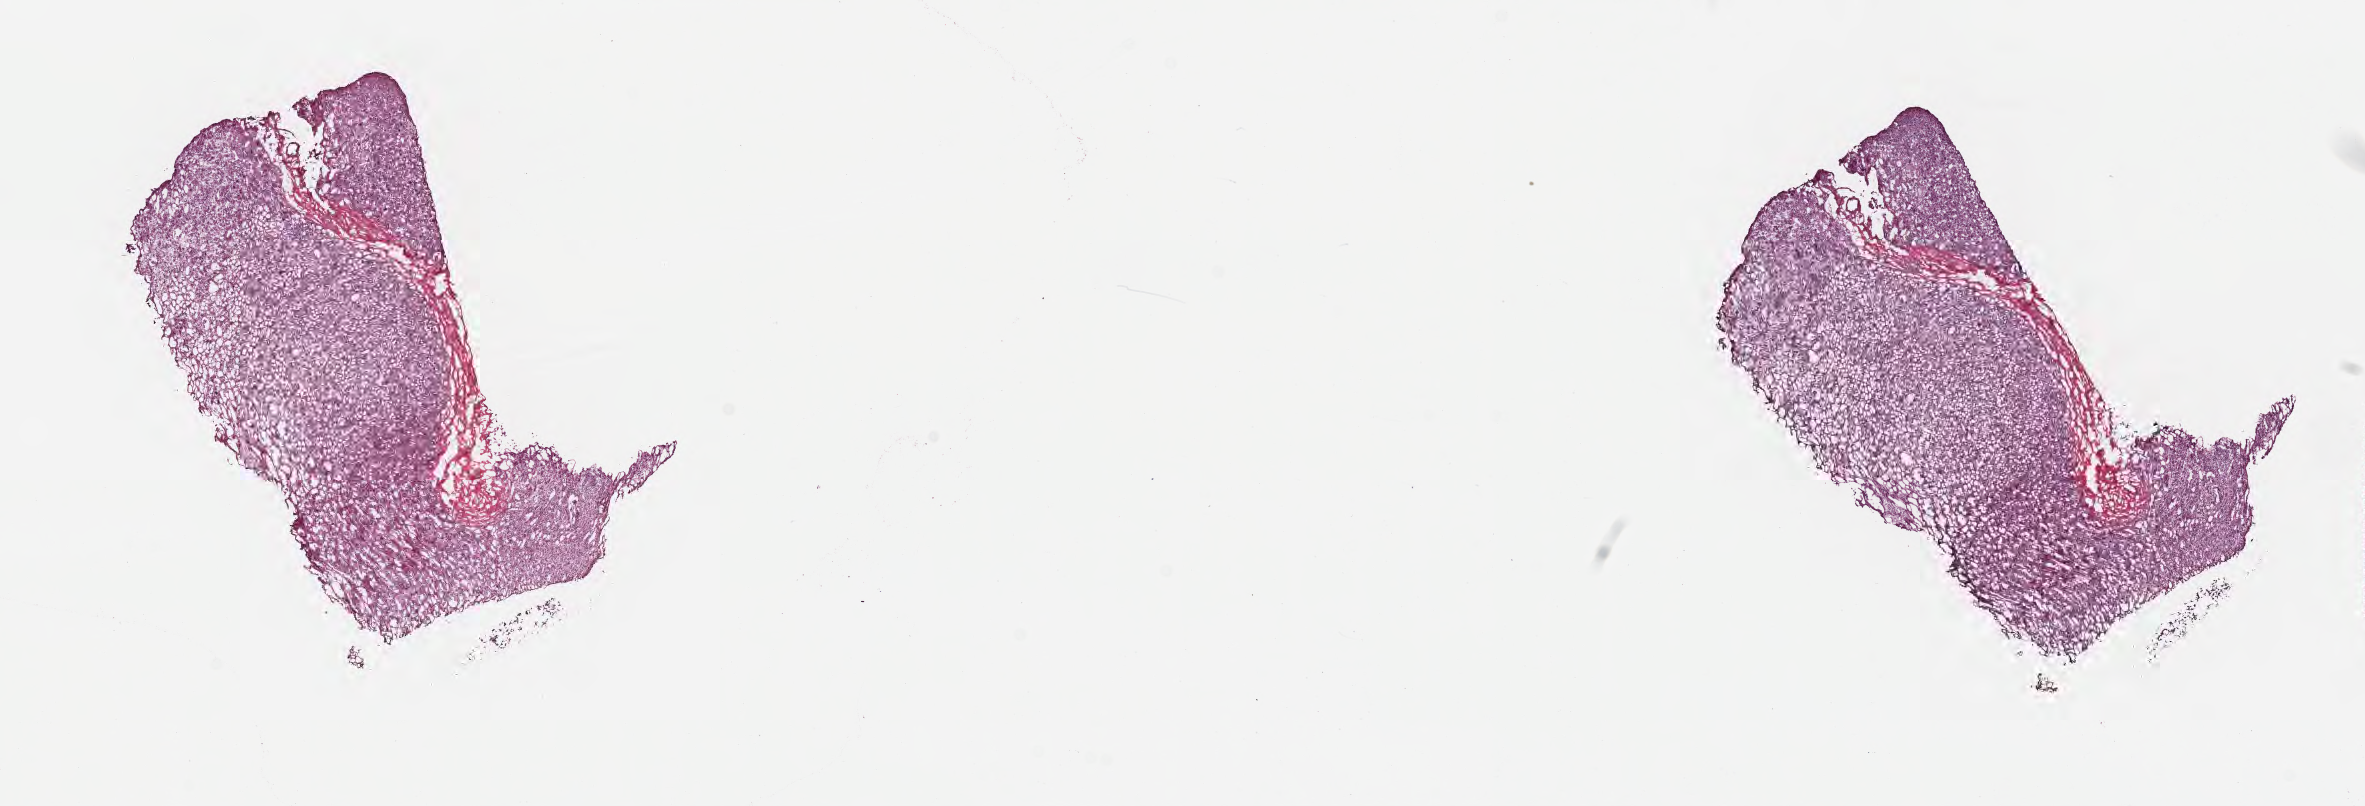
Haematoxylin and eosin whole-slide image, low-resolution overview of the scanned area, about 19.1 x 6.5 mm; frozen section (tissue freezing medium); normal-tissue sample (non-tumor) from a patient with nephroblastoma, NOS; anatomic site: kidney (left). Male patient; age at initial diagnosis 0 years. Pathologist review of this section (percent, as recorded): tumor cells 0%, tumor nuclei 0%.
This section: non-tumor tissue sample; the patient's diagnosis is given above.